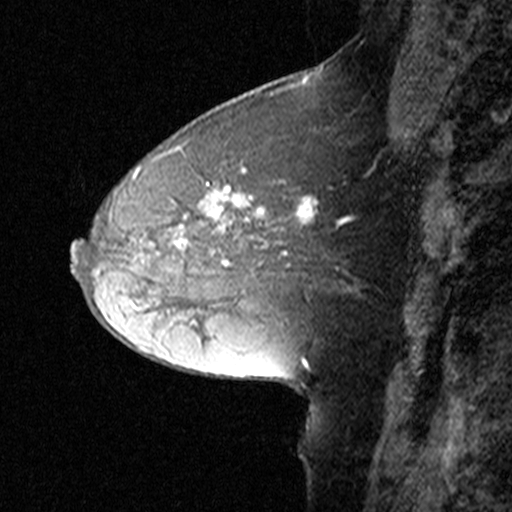
Breast MRI (dynamic contrast-enhanced), one sagittal slice; slice 19 of 44 in the series (ordered by position); dynamic contrast-enhanced study with each time point stored as its own series, time point 2 of 3 at this slice position (early post-contrast, ordered by acquisition time); 1.5 T; TE 4.5 ms, TR 11 ms; 3 mm slice thickness; 512 × 512 image matrix, field of view 200 × 200 mm. Female patient, age 50 years. From the clinical record (not read from this slice): setting: breast cancer imaged before/during neoadjuvant chemotherapy; receptor status: HR-positive, HER2-negative.
Annotated regions visible in this slice (semi-automatically segmented with operator editing):
- analysis volume of interest (the breast-tissue region the enhancement analysis was run in; not a lesion): bounding box <126,162,326,291> (left, top, right, bottom; pixels)
- tumour enhancement mask (voxels above the 90 % enhancement threshold inside the analysis volume of interest): <133,168,318,246>